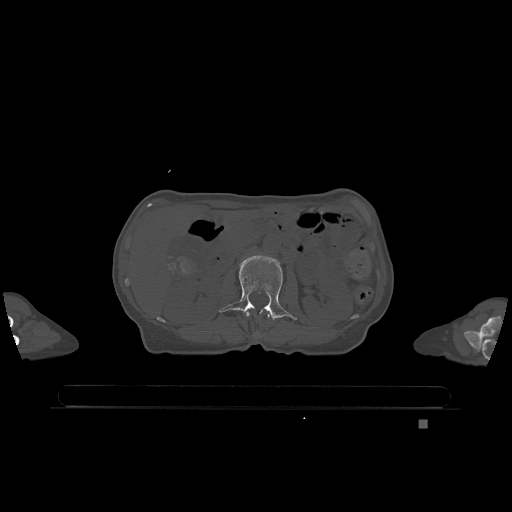
CT including the spine, one axial slice; slice 422 of 1317 in the series (ordered by position); bone window (W 1800 / L 400 HU); 0.5 mm slice thickness; 512 × 512 image matrix, field of view 500 × 500 mm. Patient: female, 74 years. Case-level facts recorded for this patient, not image findings: primary cancer: lung; vertebrae with lytic lesions (as recorded): T1, T4, T5, T6, L4, L5.
Outlined on this slice (semi-automatic segmentation, software-assisted and operator-edited):
- L1 vertebra: bounding box [x1, y1, x2, y2] px = [246, 312, 270, 318]
- L2 vertebra: [219, 255, 297, 320]